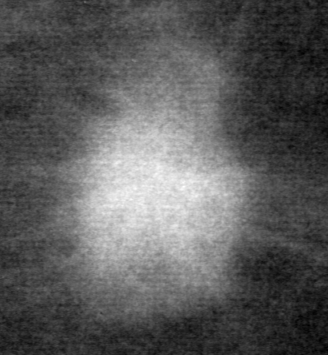
Region of interest cut from a scanned film mammogram (one marked finding), left breast, CC view.
Finding: mass, shape irregular, margins spiculated; BI-RADS assessment category 5; pathology result (as recorded, not read from the image): malignant.